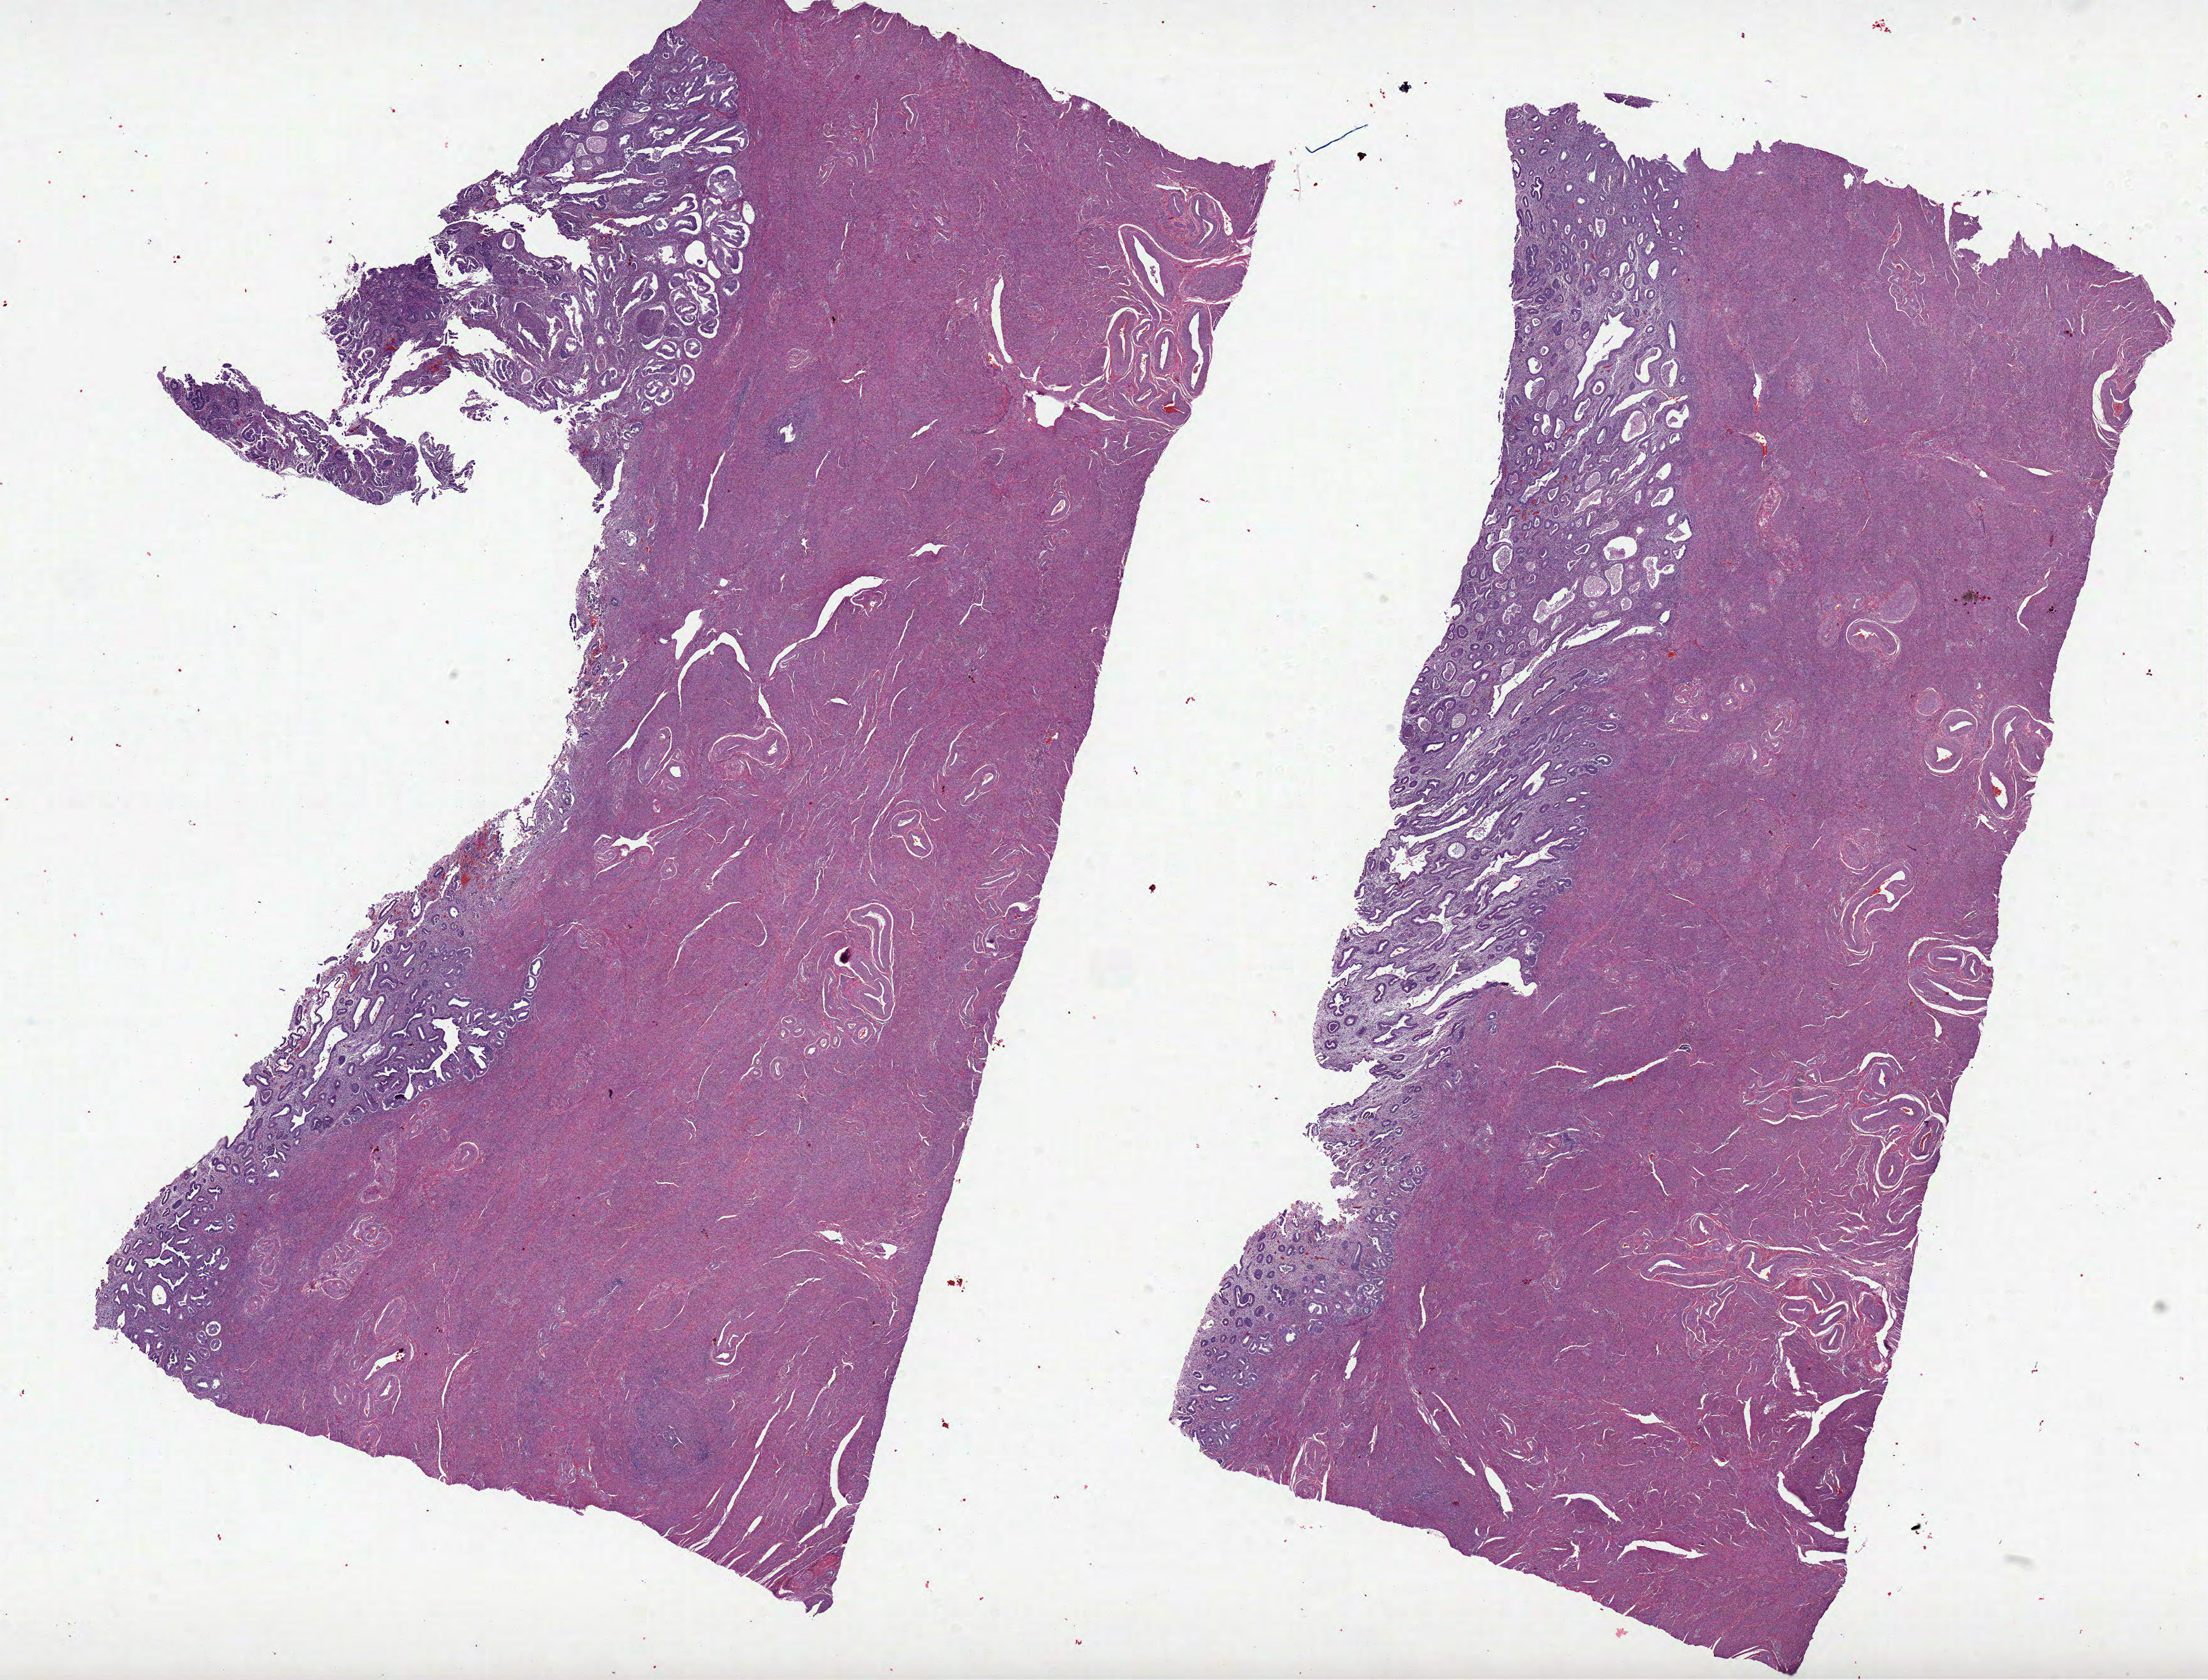
Whole-slide histology image, H&E — low-resolution overview of the scanned area, about 27.8 x 21.2 mm (slide scanned at 20x); formalin-fixed paraffin-embedded (FFPE) diagnostic section; primary tumour sample from the uterus. Female patient; age at initial diagnosis 45 years. Histologic grade: G2 (moderately differentiated).
* histologic diagnosis: Endometrioid adenocarcinoma, NOS (endometrium)
* FIGO stage: IA